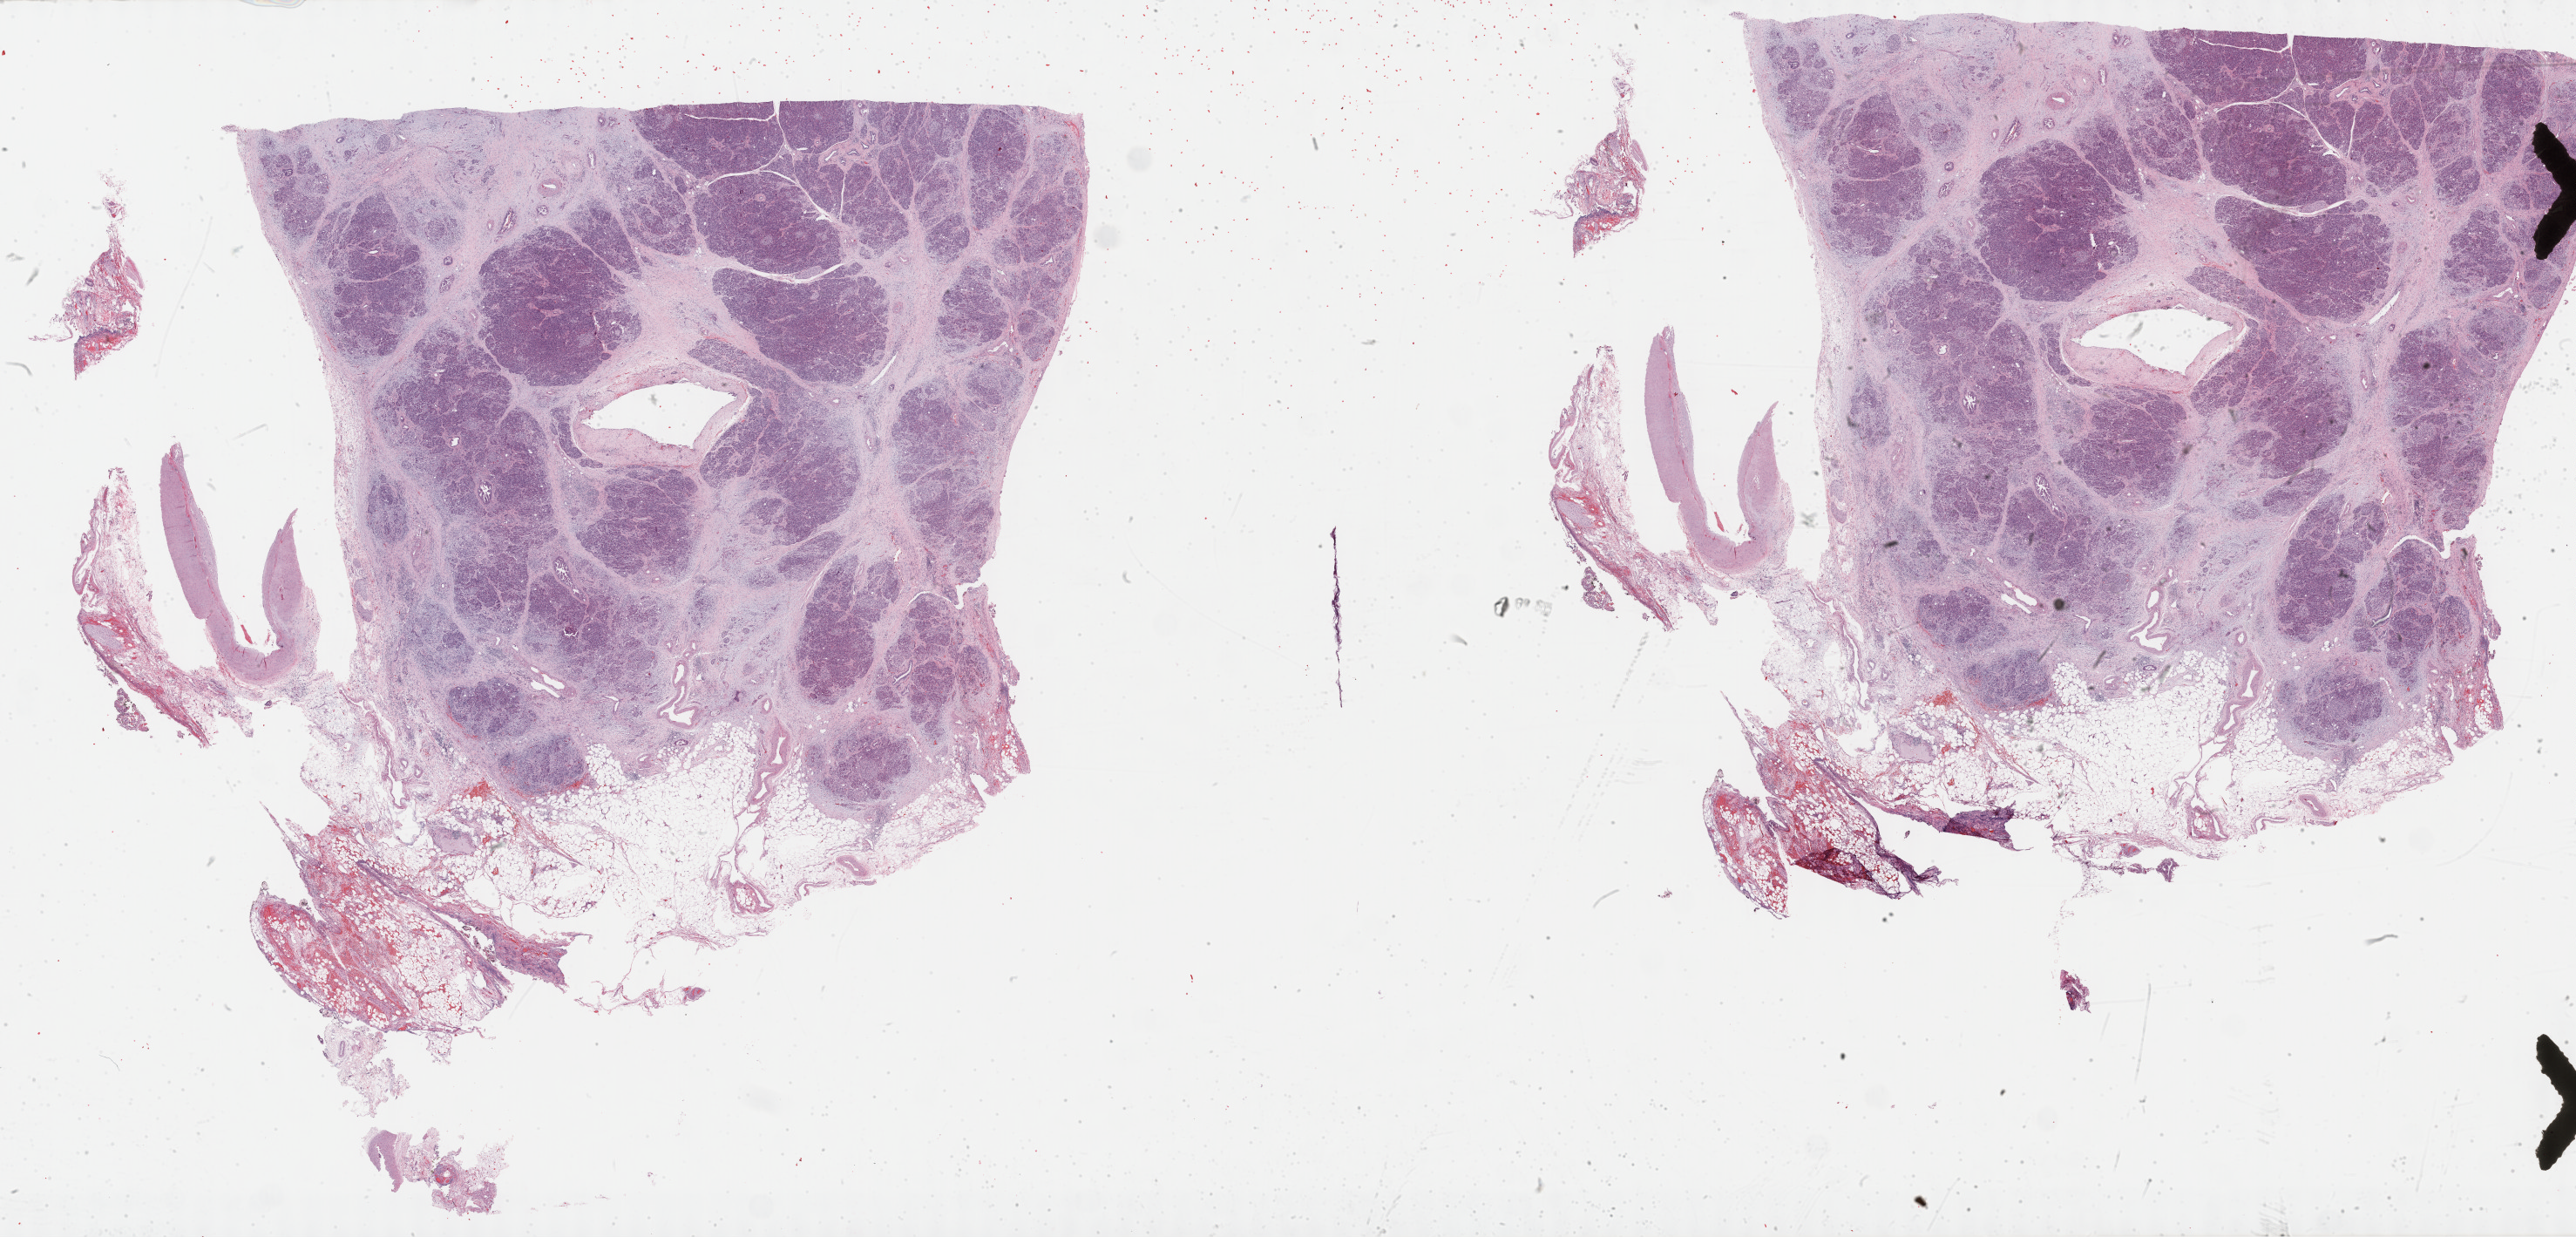
Digitized Hematoxylin and eosin (H&E) stained tissue section (whole slide) — a low-resolution overview of the entire scanned area, about 47.8 x 23.0 mm (slide scanned at 40x). FFPE section. Sample: primary tumour, pancreas. Female patient; age at initial diagnosis 73 years. Histologic grade: G2 (moderately differentiated).
AJCC pathologic stage: III (5th edition). Diagnosis: Infiltrating duct carcinoma, NOS (head of pancreas).